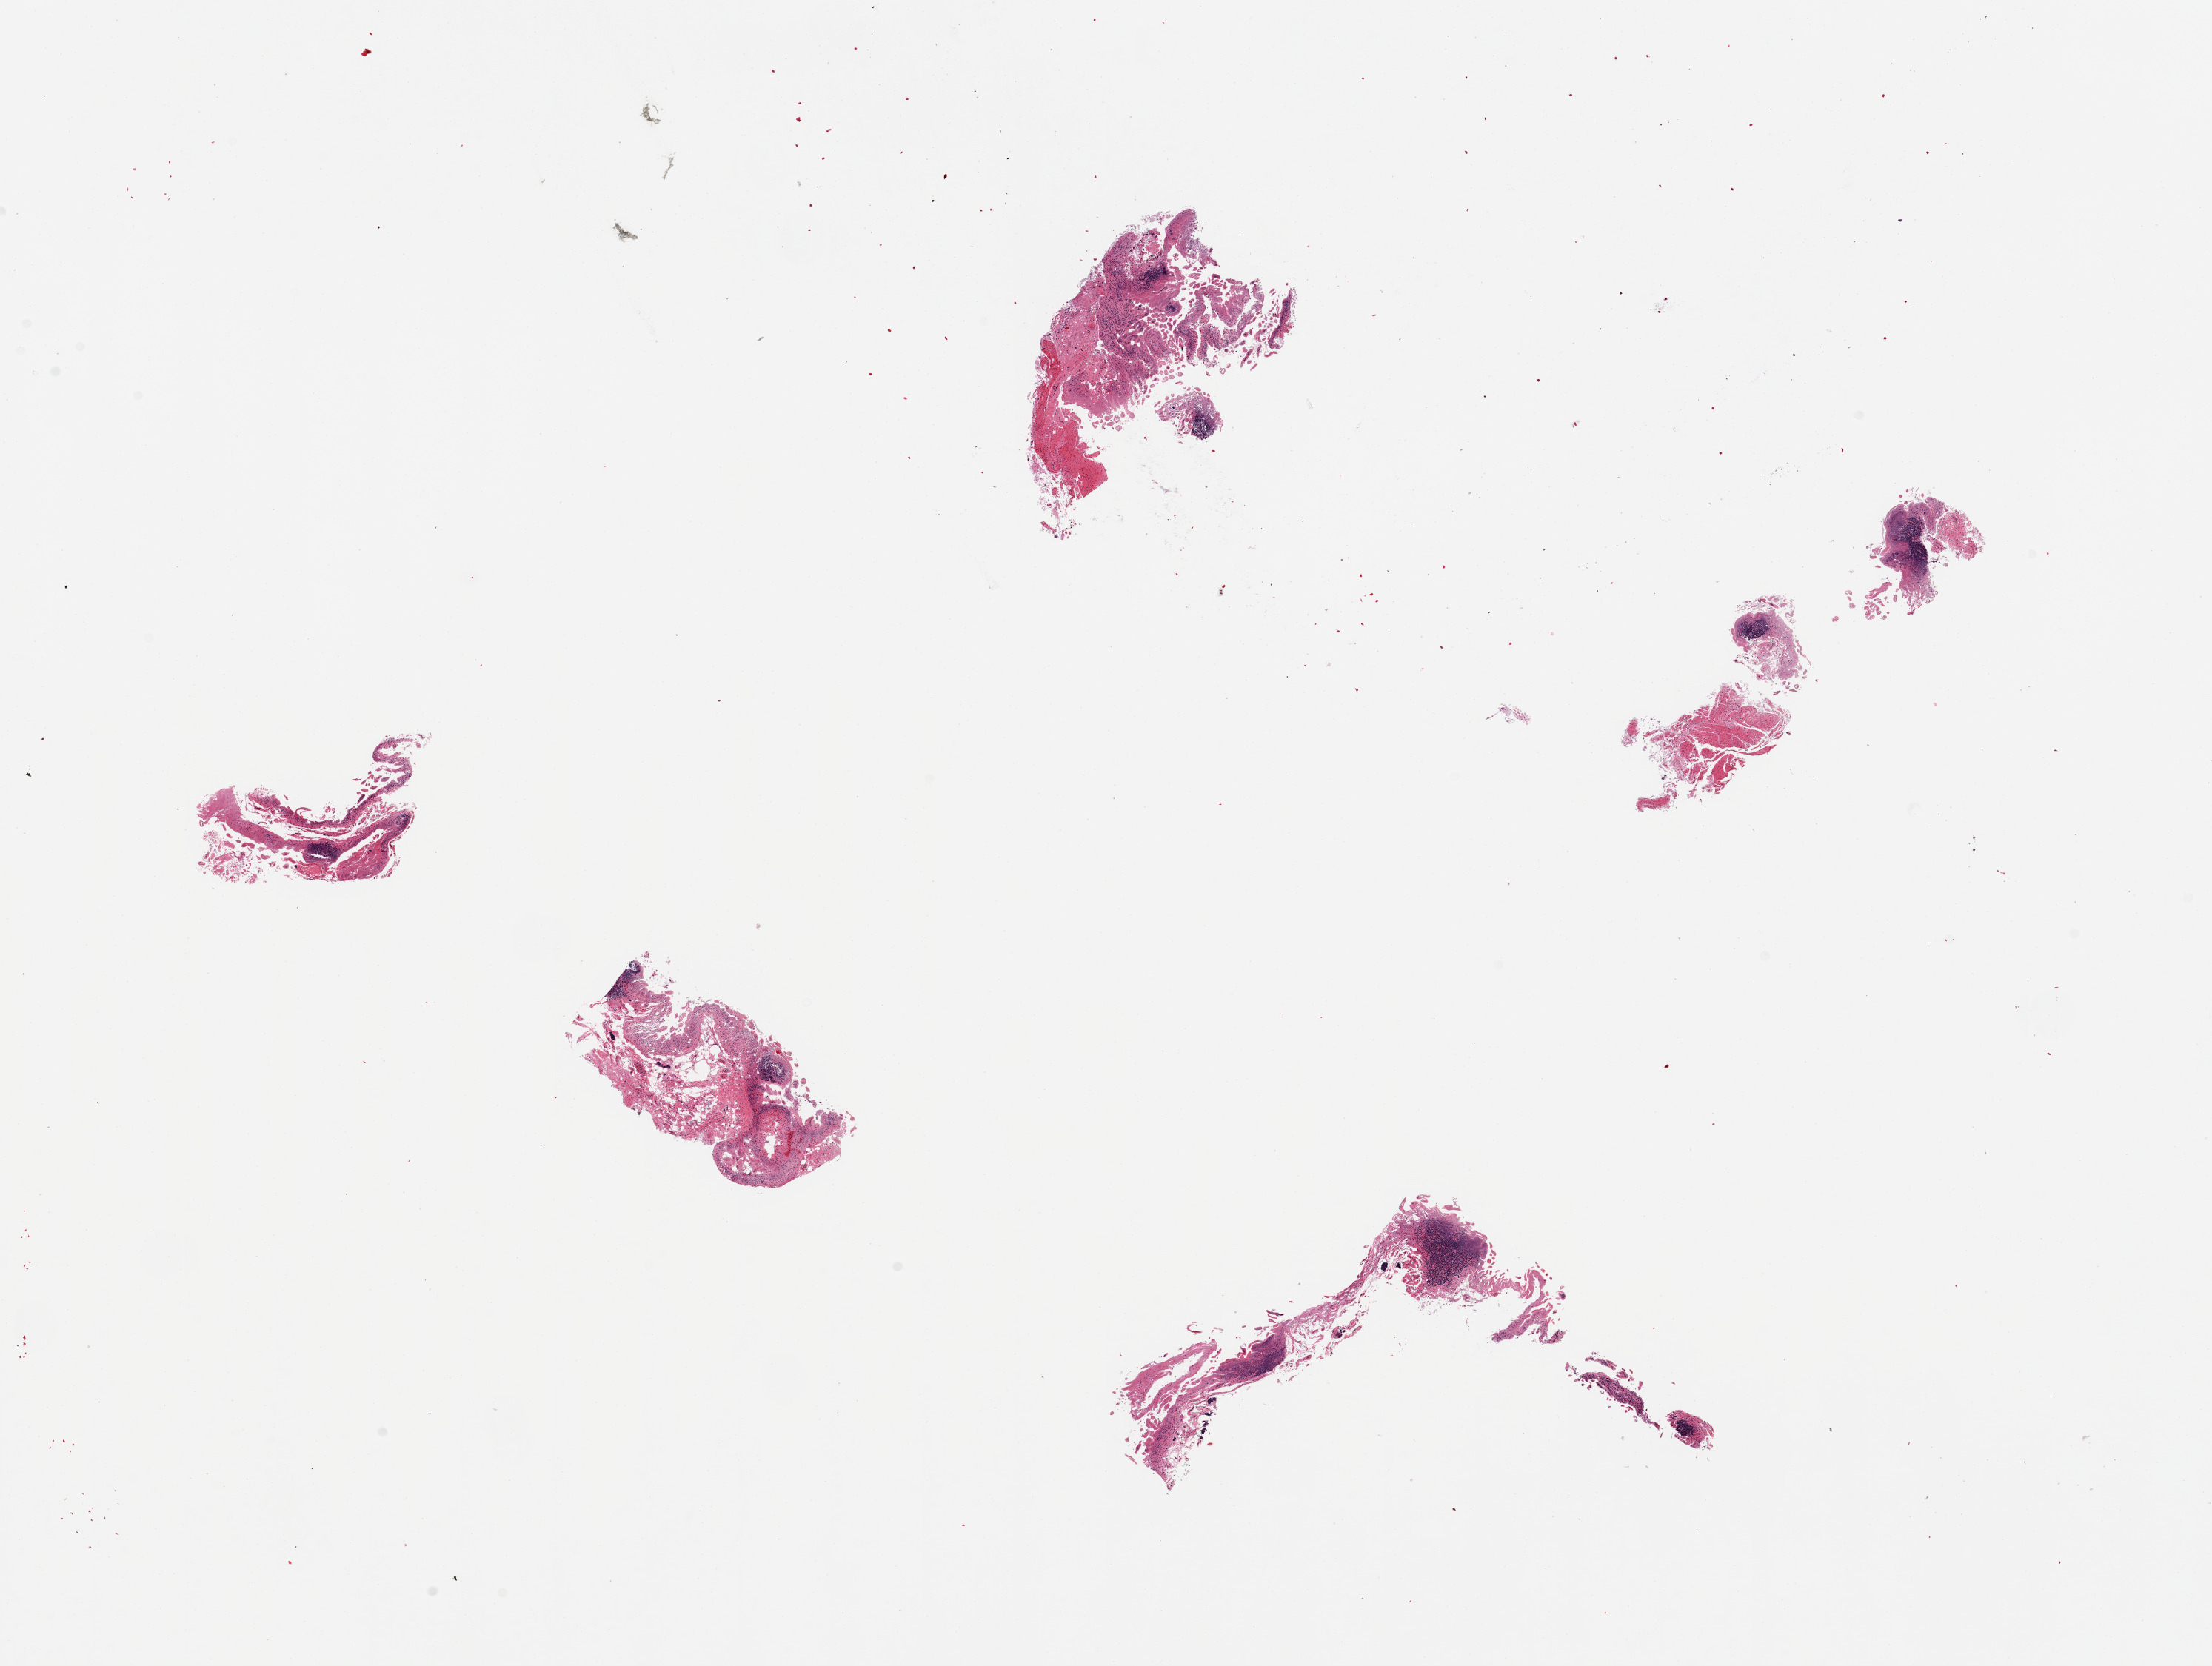
Hematoxylin and eosin (H&E) whole-slide image, whole scanned area (about 23.6 x 17.8 mm, slide scanned at 20x) shown as a low-resolution overview. Female donor.
Specimen: PAXgene-fixed paraffin-embedded (PFPE) section; section of ileum (target tissue); tissue donor sample.